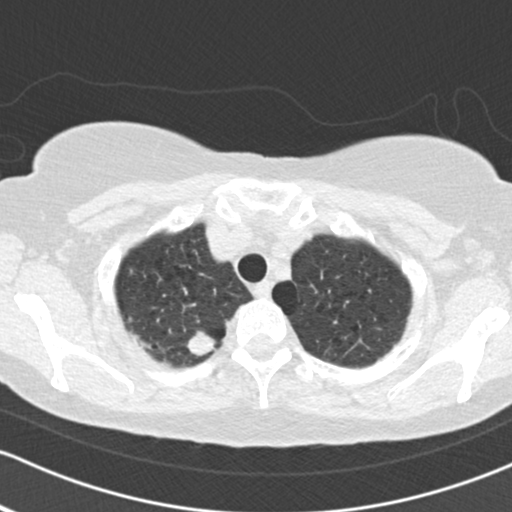
Low-dose screening chest CT, axial slice; second annual screen; lung window (W 1500 / L -600 HU); 2 mm slice thickness; slice 19 of 161 in the series; 512 × 512 image matrix. Female participant, aged 64 years at enrolment. Current smoker at enrolment.
• Expert reader's lesion annotation, bounding box <172,323,223,370> (left, top, right, bottom; pixels).
• The exam's reader record, not a measurement of the box and not confirmed to be the same lesion: non-calcified nodule or mass ≥4 mm, right upper lobe, 16 × 15 mm, spiculated (stellate) margins, soft tissue attenuation, pre-existing on the prior screen: no.
• Participant outcome: lung cancer diagnosed 45 days after this screen — adenocarcinoma, NOS, right upper lobe, poorly differentiated (G3), stage IB (AJCC 6th edition), 15 mm at pathology.